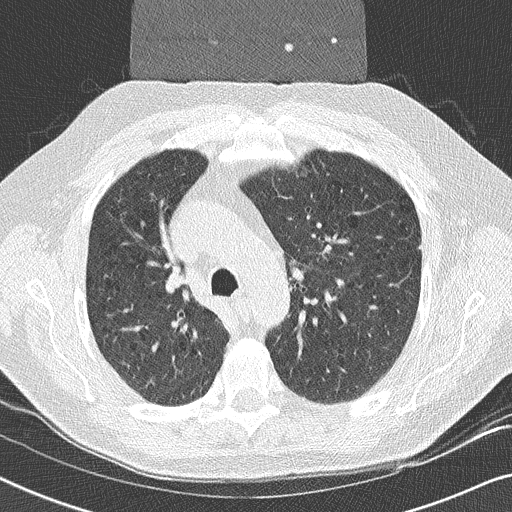
Low-dose screening chest CT, axial slice. Second screening round (one year after baseline). Lung window (W 1500 / L -600 HU). 120 kVp. 512 × 512 image matrix, field of view 330 × 330 mm. Male, age 59 years at enrolment. Former smoker at enrolment.
• Expert reader's lesion annotation, bounding box <137,254,200,308> (left, top, right, bottom; pixels).
• Screening reader's record for this exam (one nodule recorded; not confirmed to be the boxed lesion): non-calcified nodule or mass ≥4 mm, right upper lobe, 17 × 16 mm, smooth margins, soft tissue attenuation, pre-existing on the prior screen: yes.
• Official screen result: positive, other.
• Later outcome: lung cancer diagnosed 14 days after this screen — squamous cell carcinoma, NOS, right upper lobe, poorly differentiated (G3), stage IIA (AJCC 6th edition), 20 mm at pathology.